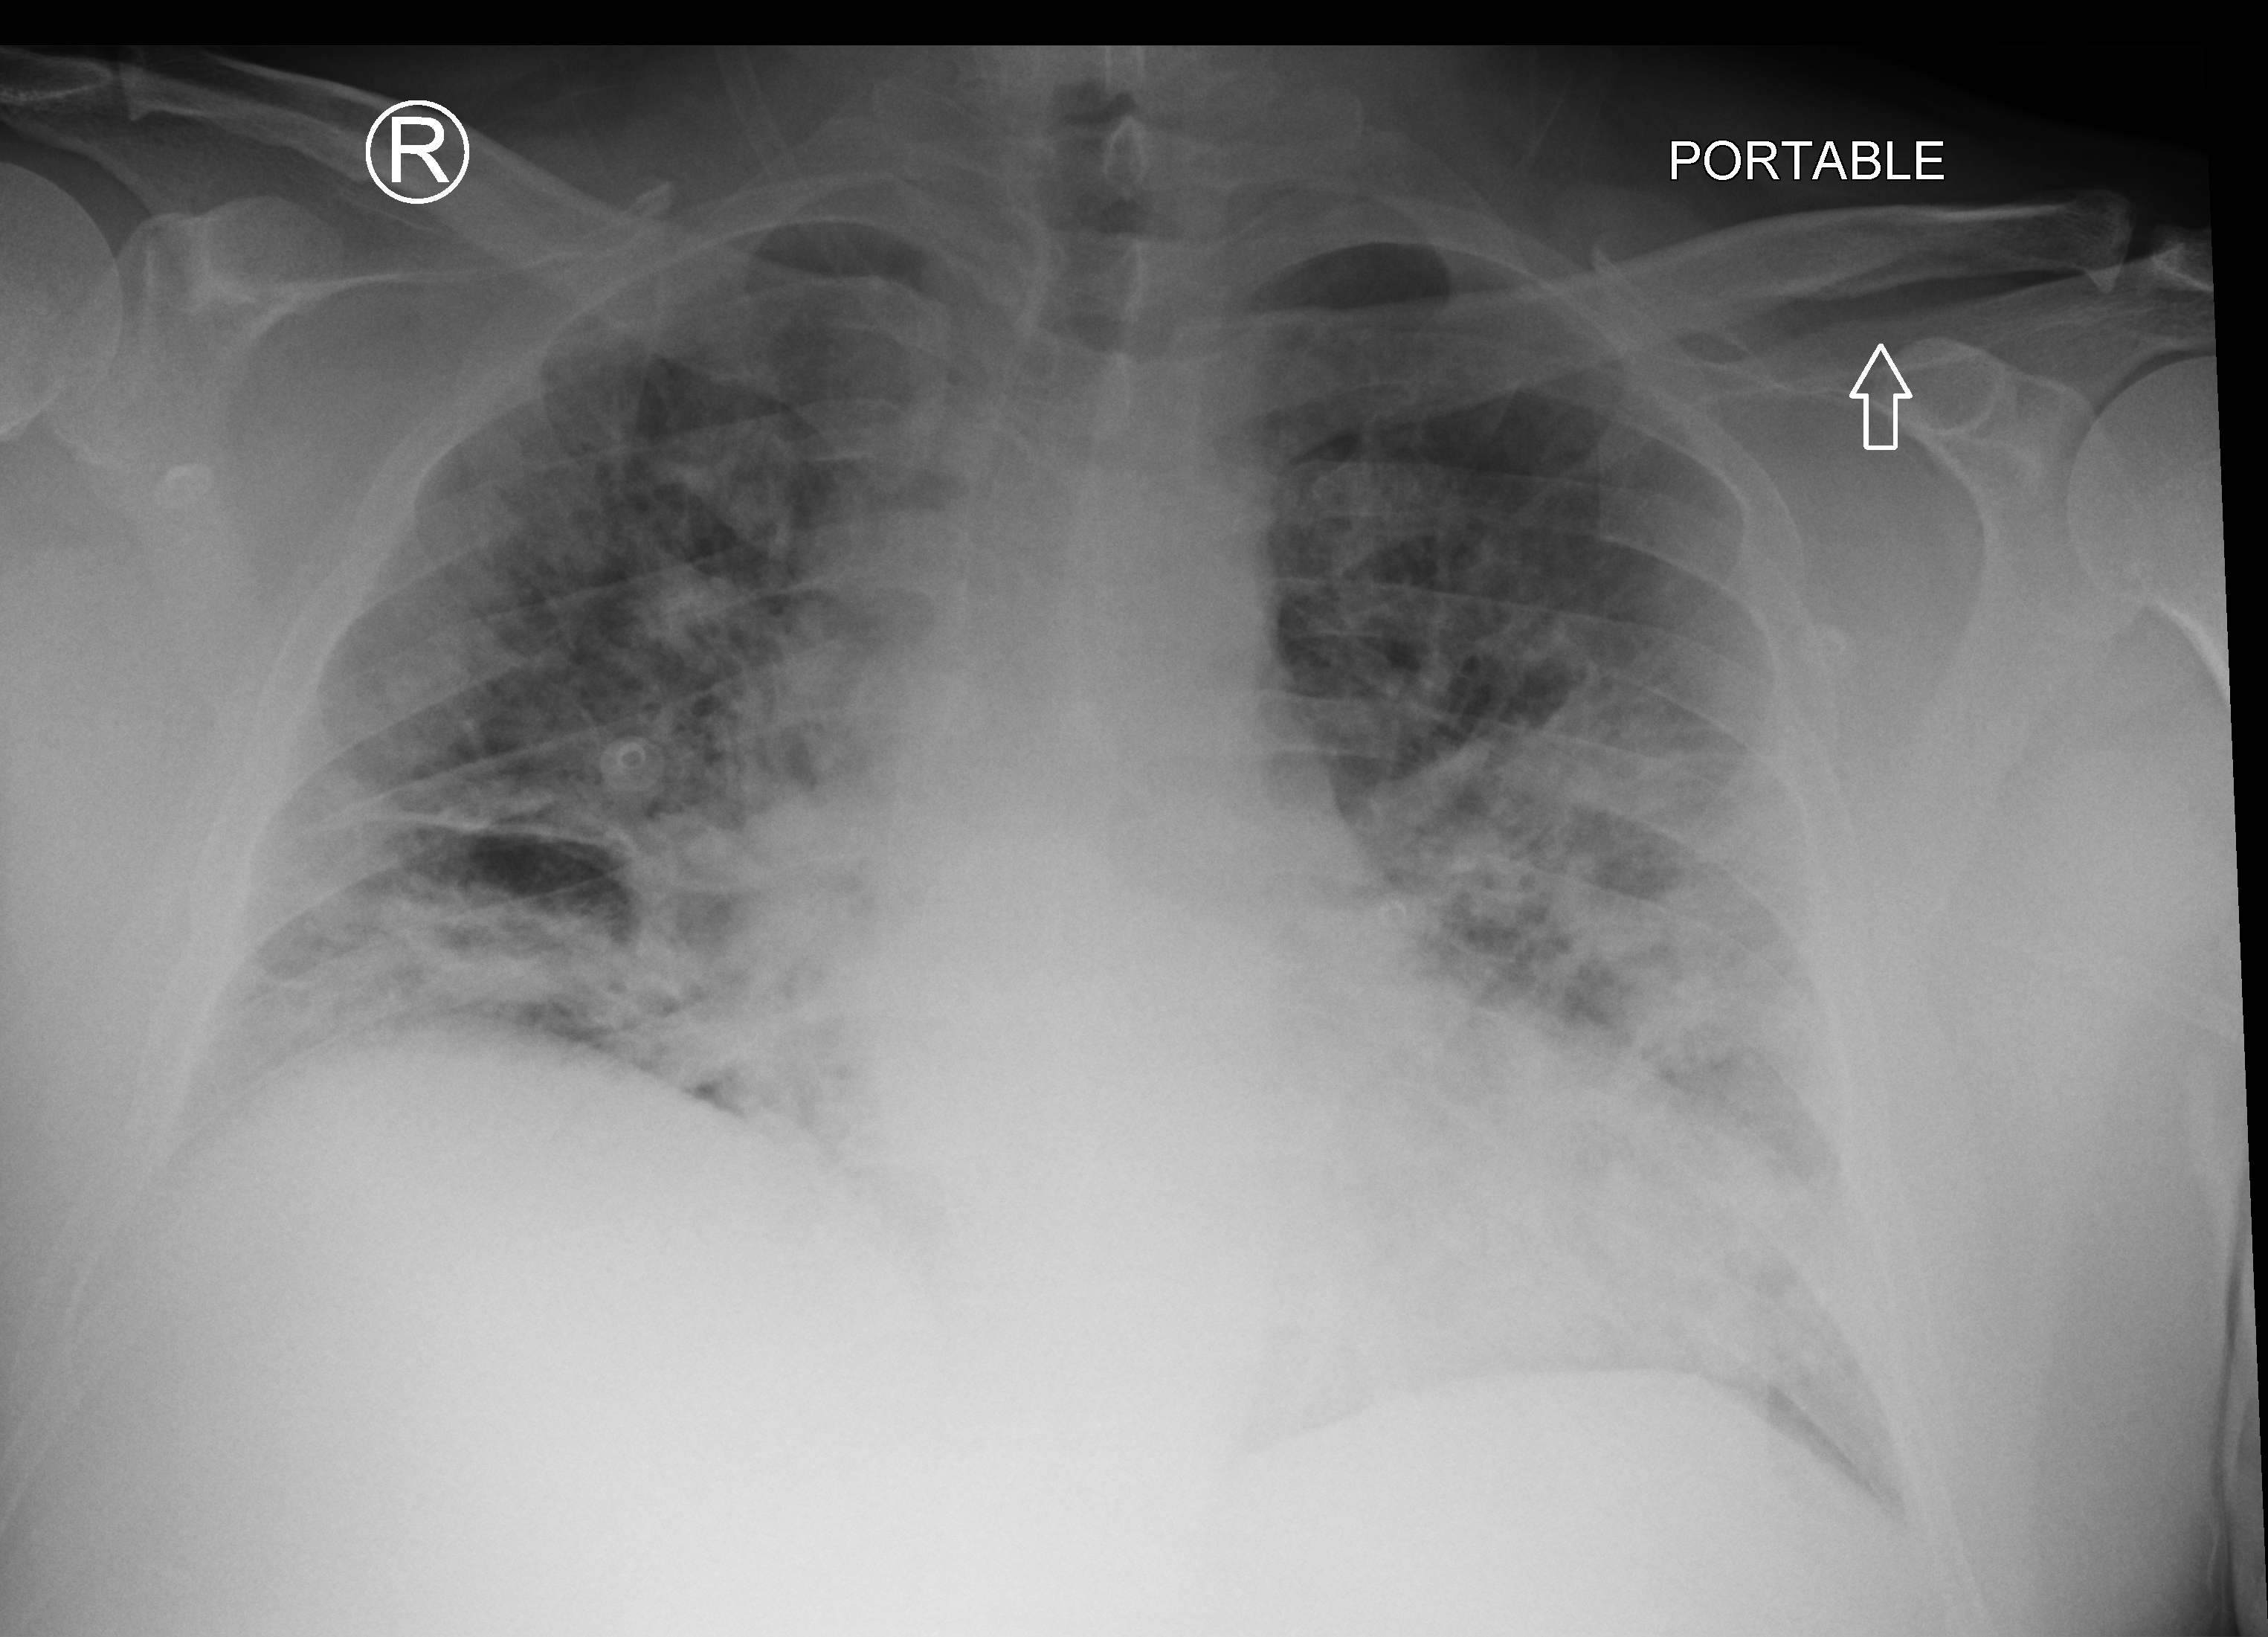
Chest X-ray (portable); anteroposterior (AP) projection. Male patient hospitalised with COVID-19, age 18–59 years.
Hospital-stay facts (about this admission, not read from this image; timing relative to this image not recorded):
- diabetes (admission record): yes
- mechanically ventilated during this hospital stay: yes